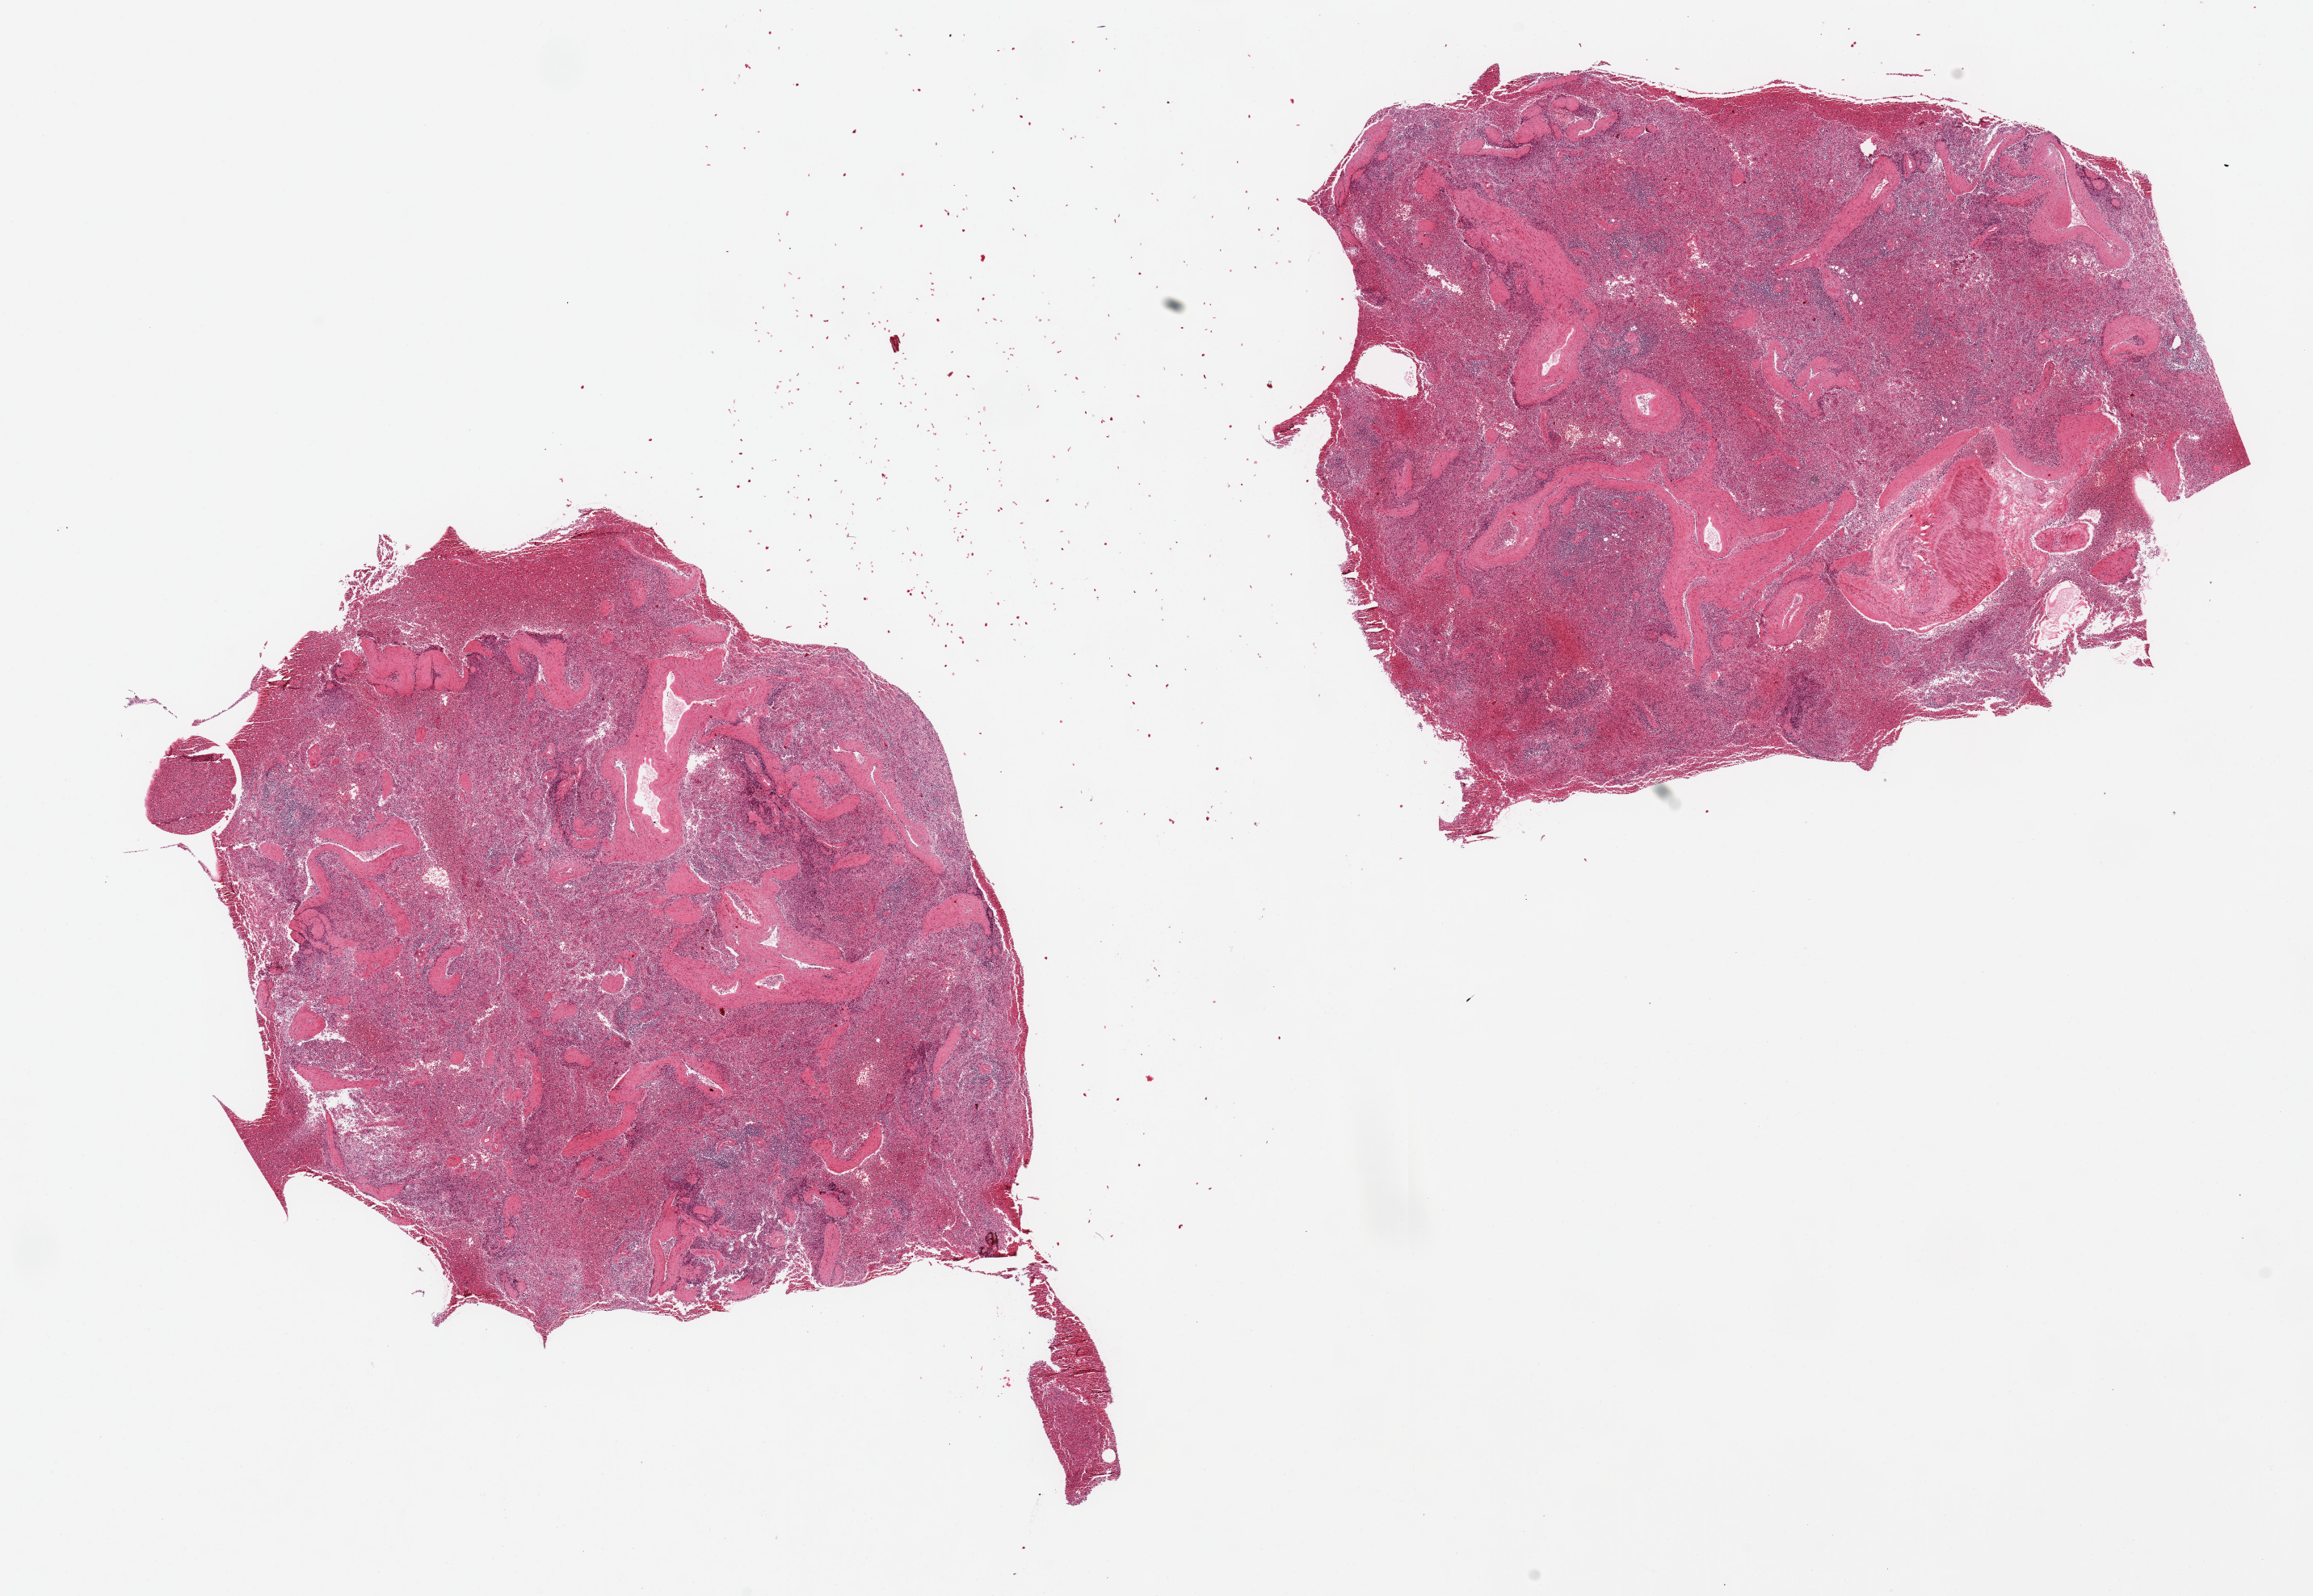
Digitized haematoxylin and eosin-stained section, brightfield, whole scanned area (about 22.6 x 15.6 mm, slide scanned at 20x) shown as a low-resolution overview; PAXgene-fixed paraffin-embedded (PFPE) section; section of spleen (target tissue); tissue donor sample.
Review note (as recorded): 2 pieces, 11x8 & 9x7.5mm.